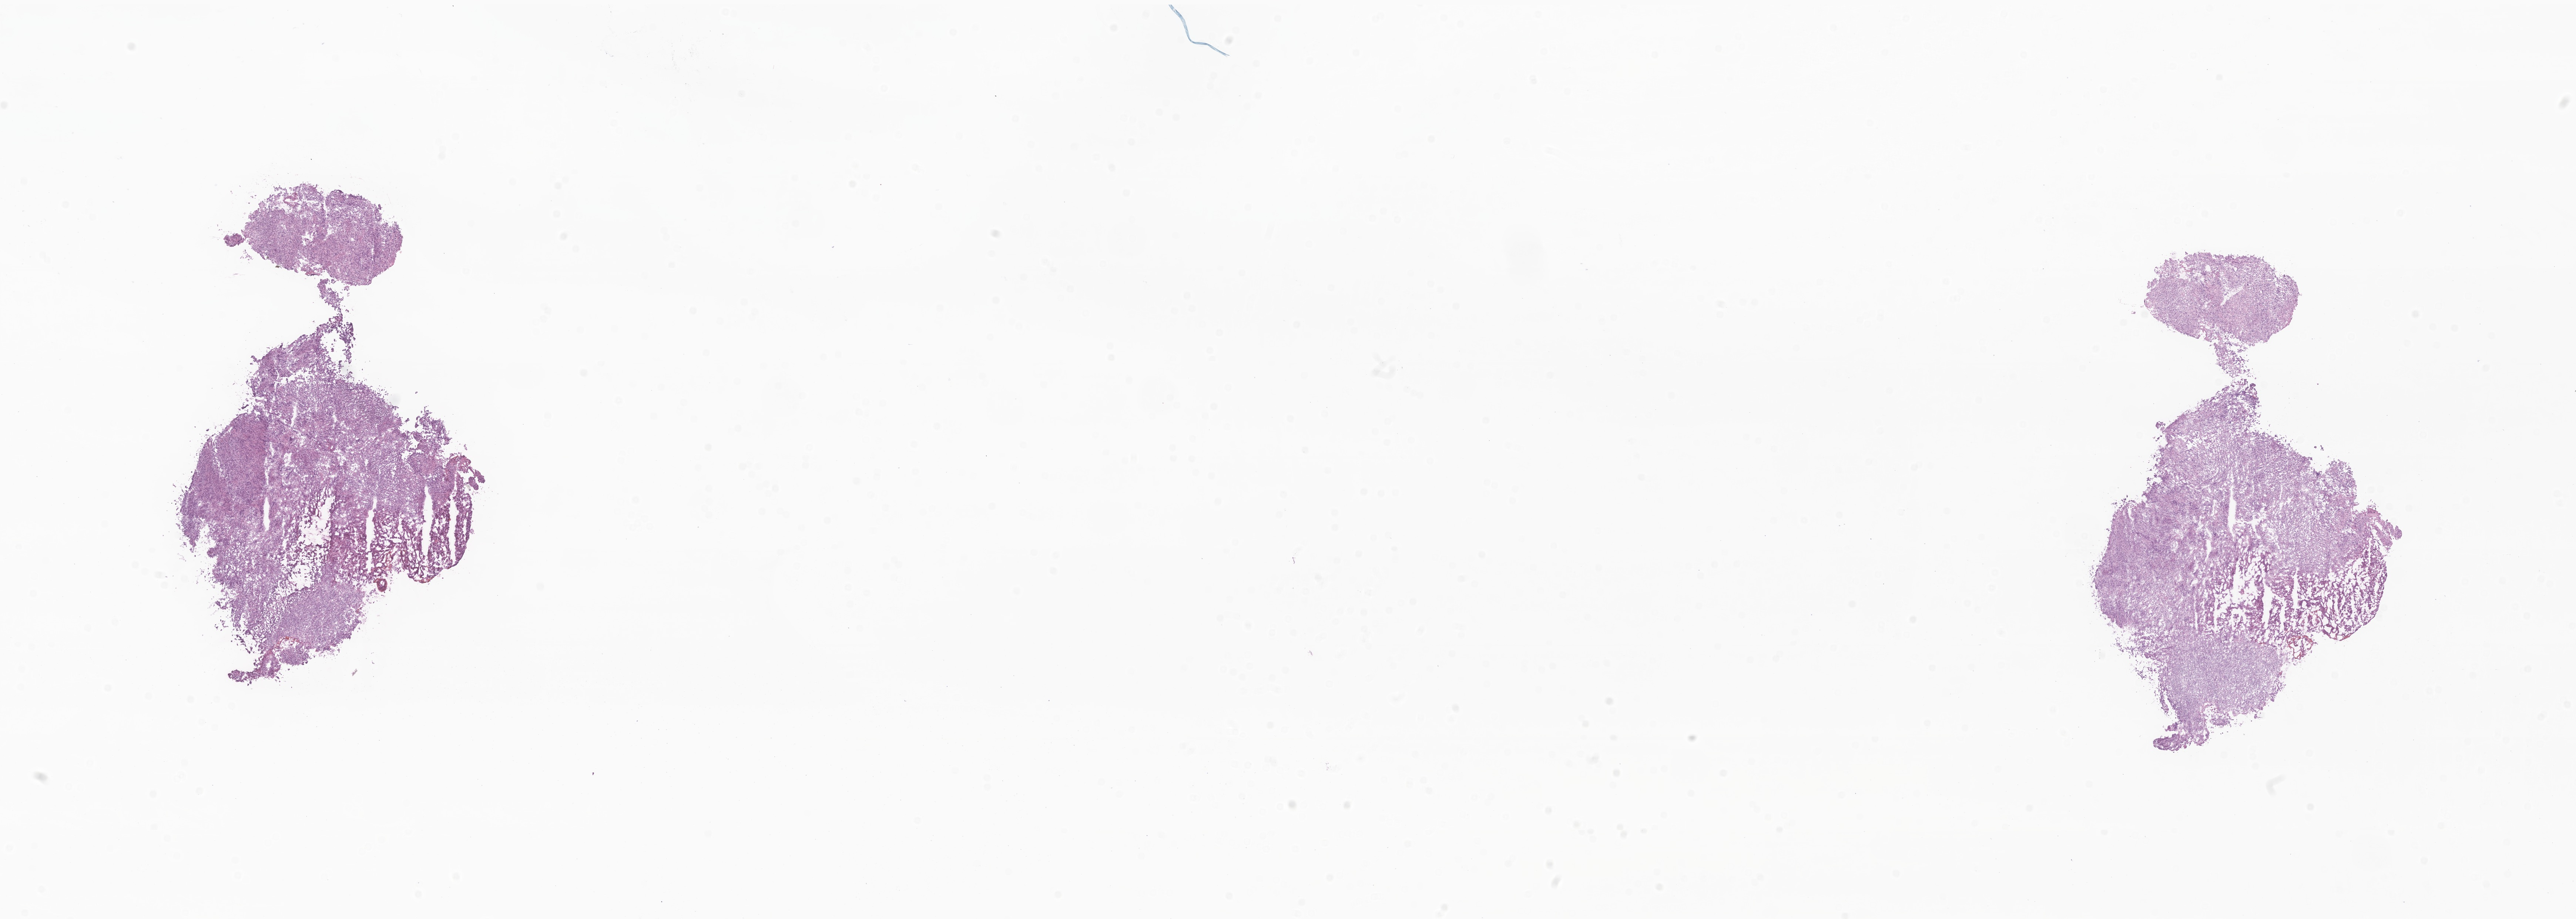
Whole-slide image, haematoxylin and eosin stain of tumor tissue from the brain, shown as a low-resolution overview of the whole scanned area (about 29.3 x 10.5 mm). Frozen section. Patient female; age 179 months (14 years 11 months).
Diagnosis: Mixed germ cell tumor.